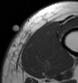
MRI of an extremity soft-tissue mass, one axial slice; position 5 of 43 along the scan axis; MR volume resampled by the dataset authors to the PET/CT grid (not the native acquisition matrix); 3.27 mm slice thickness; 78 × 83 image matrix, field of view 76 × 81 mm. Male patient. From the clinical record (not read from this slice): histological type: pleiomorphic leiomyosarcoma; grade: high; site of the primary tumour: left thigh.
Annotated regions visible in this slice (expert contour drawn on MRI and transferred to this co-registered scan by the dataset authors):
- gross tumour volume including surrounding oedema: bounding box (x1, y1, x2, y2) in pixels: (34, 24, 57, 54)